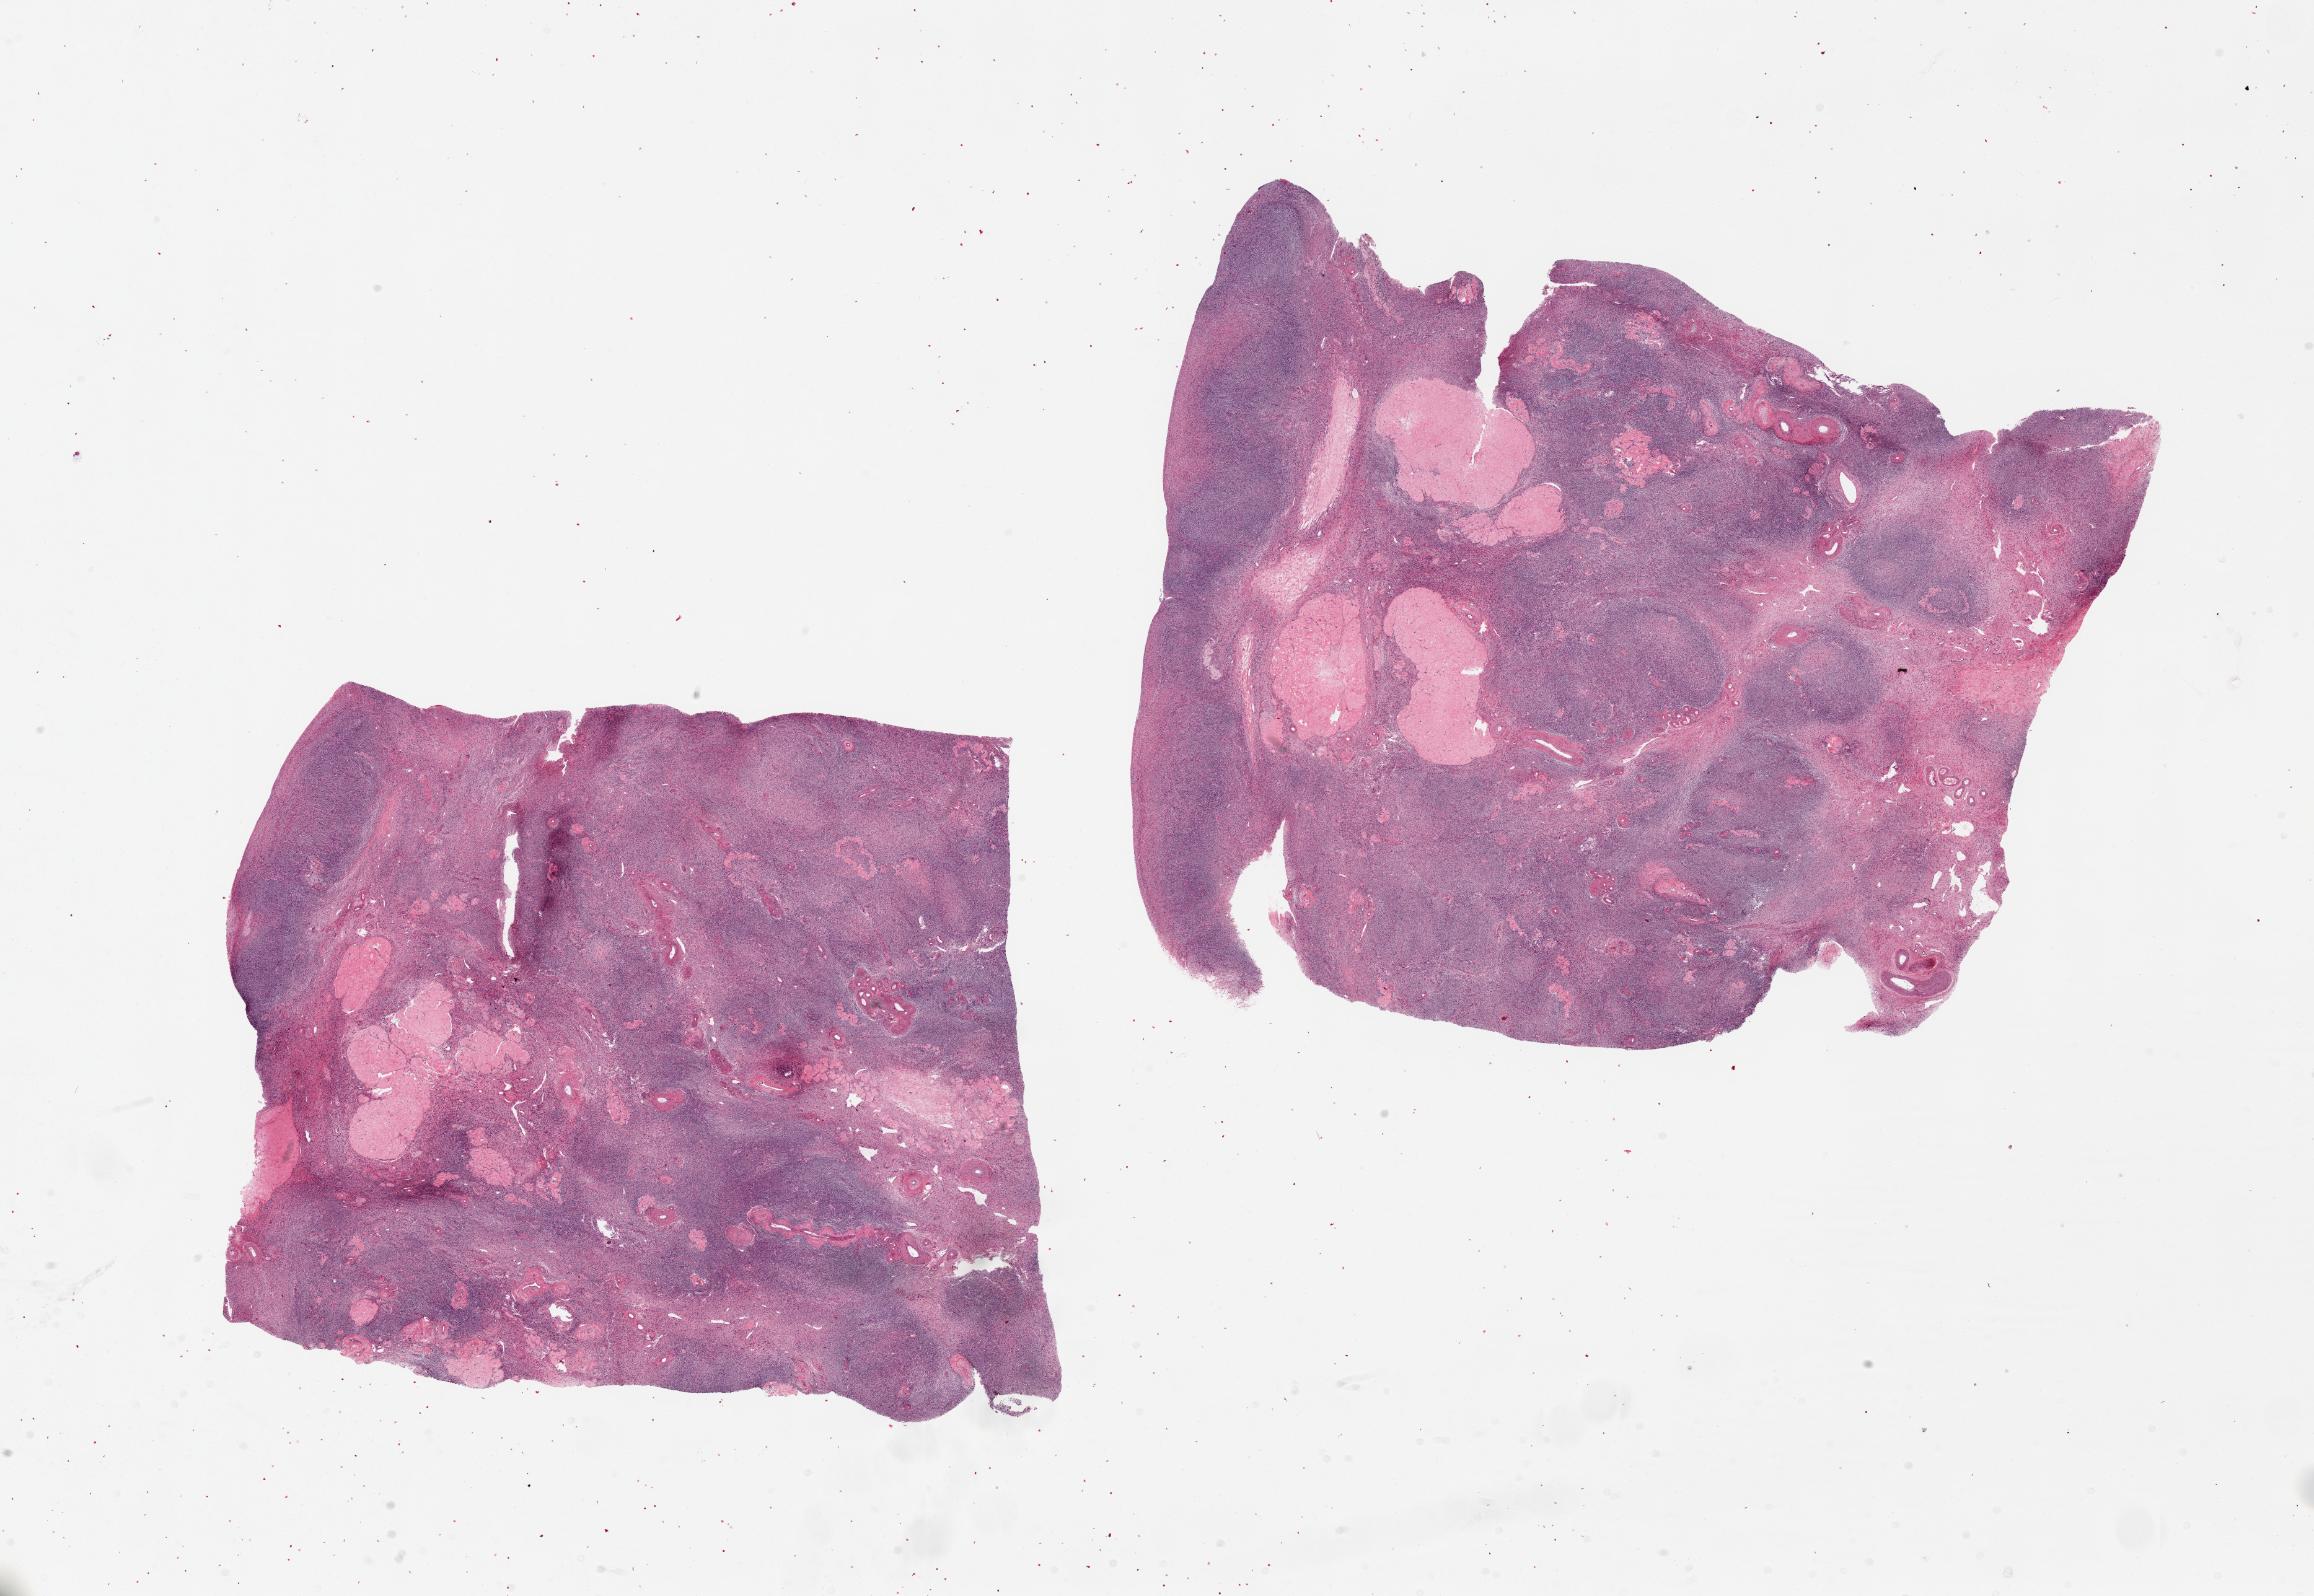
Whole-slide image, haematoxylin and eosin stain, low-resolution overview of the scanned area, about 29.5 x 20.4 mm (from a 20x scan); PAXgene-fixed paraffin-embedded (PFPE) section; sampled site (target tissue): ovary; tissue donor sample. Donor: female.
- review note (as recorded): 2 pieces, 11x9 & 12.5x11mm. Numerous corpora albicantia